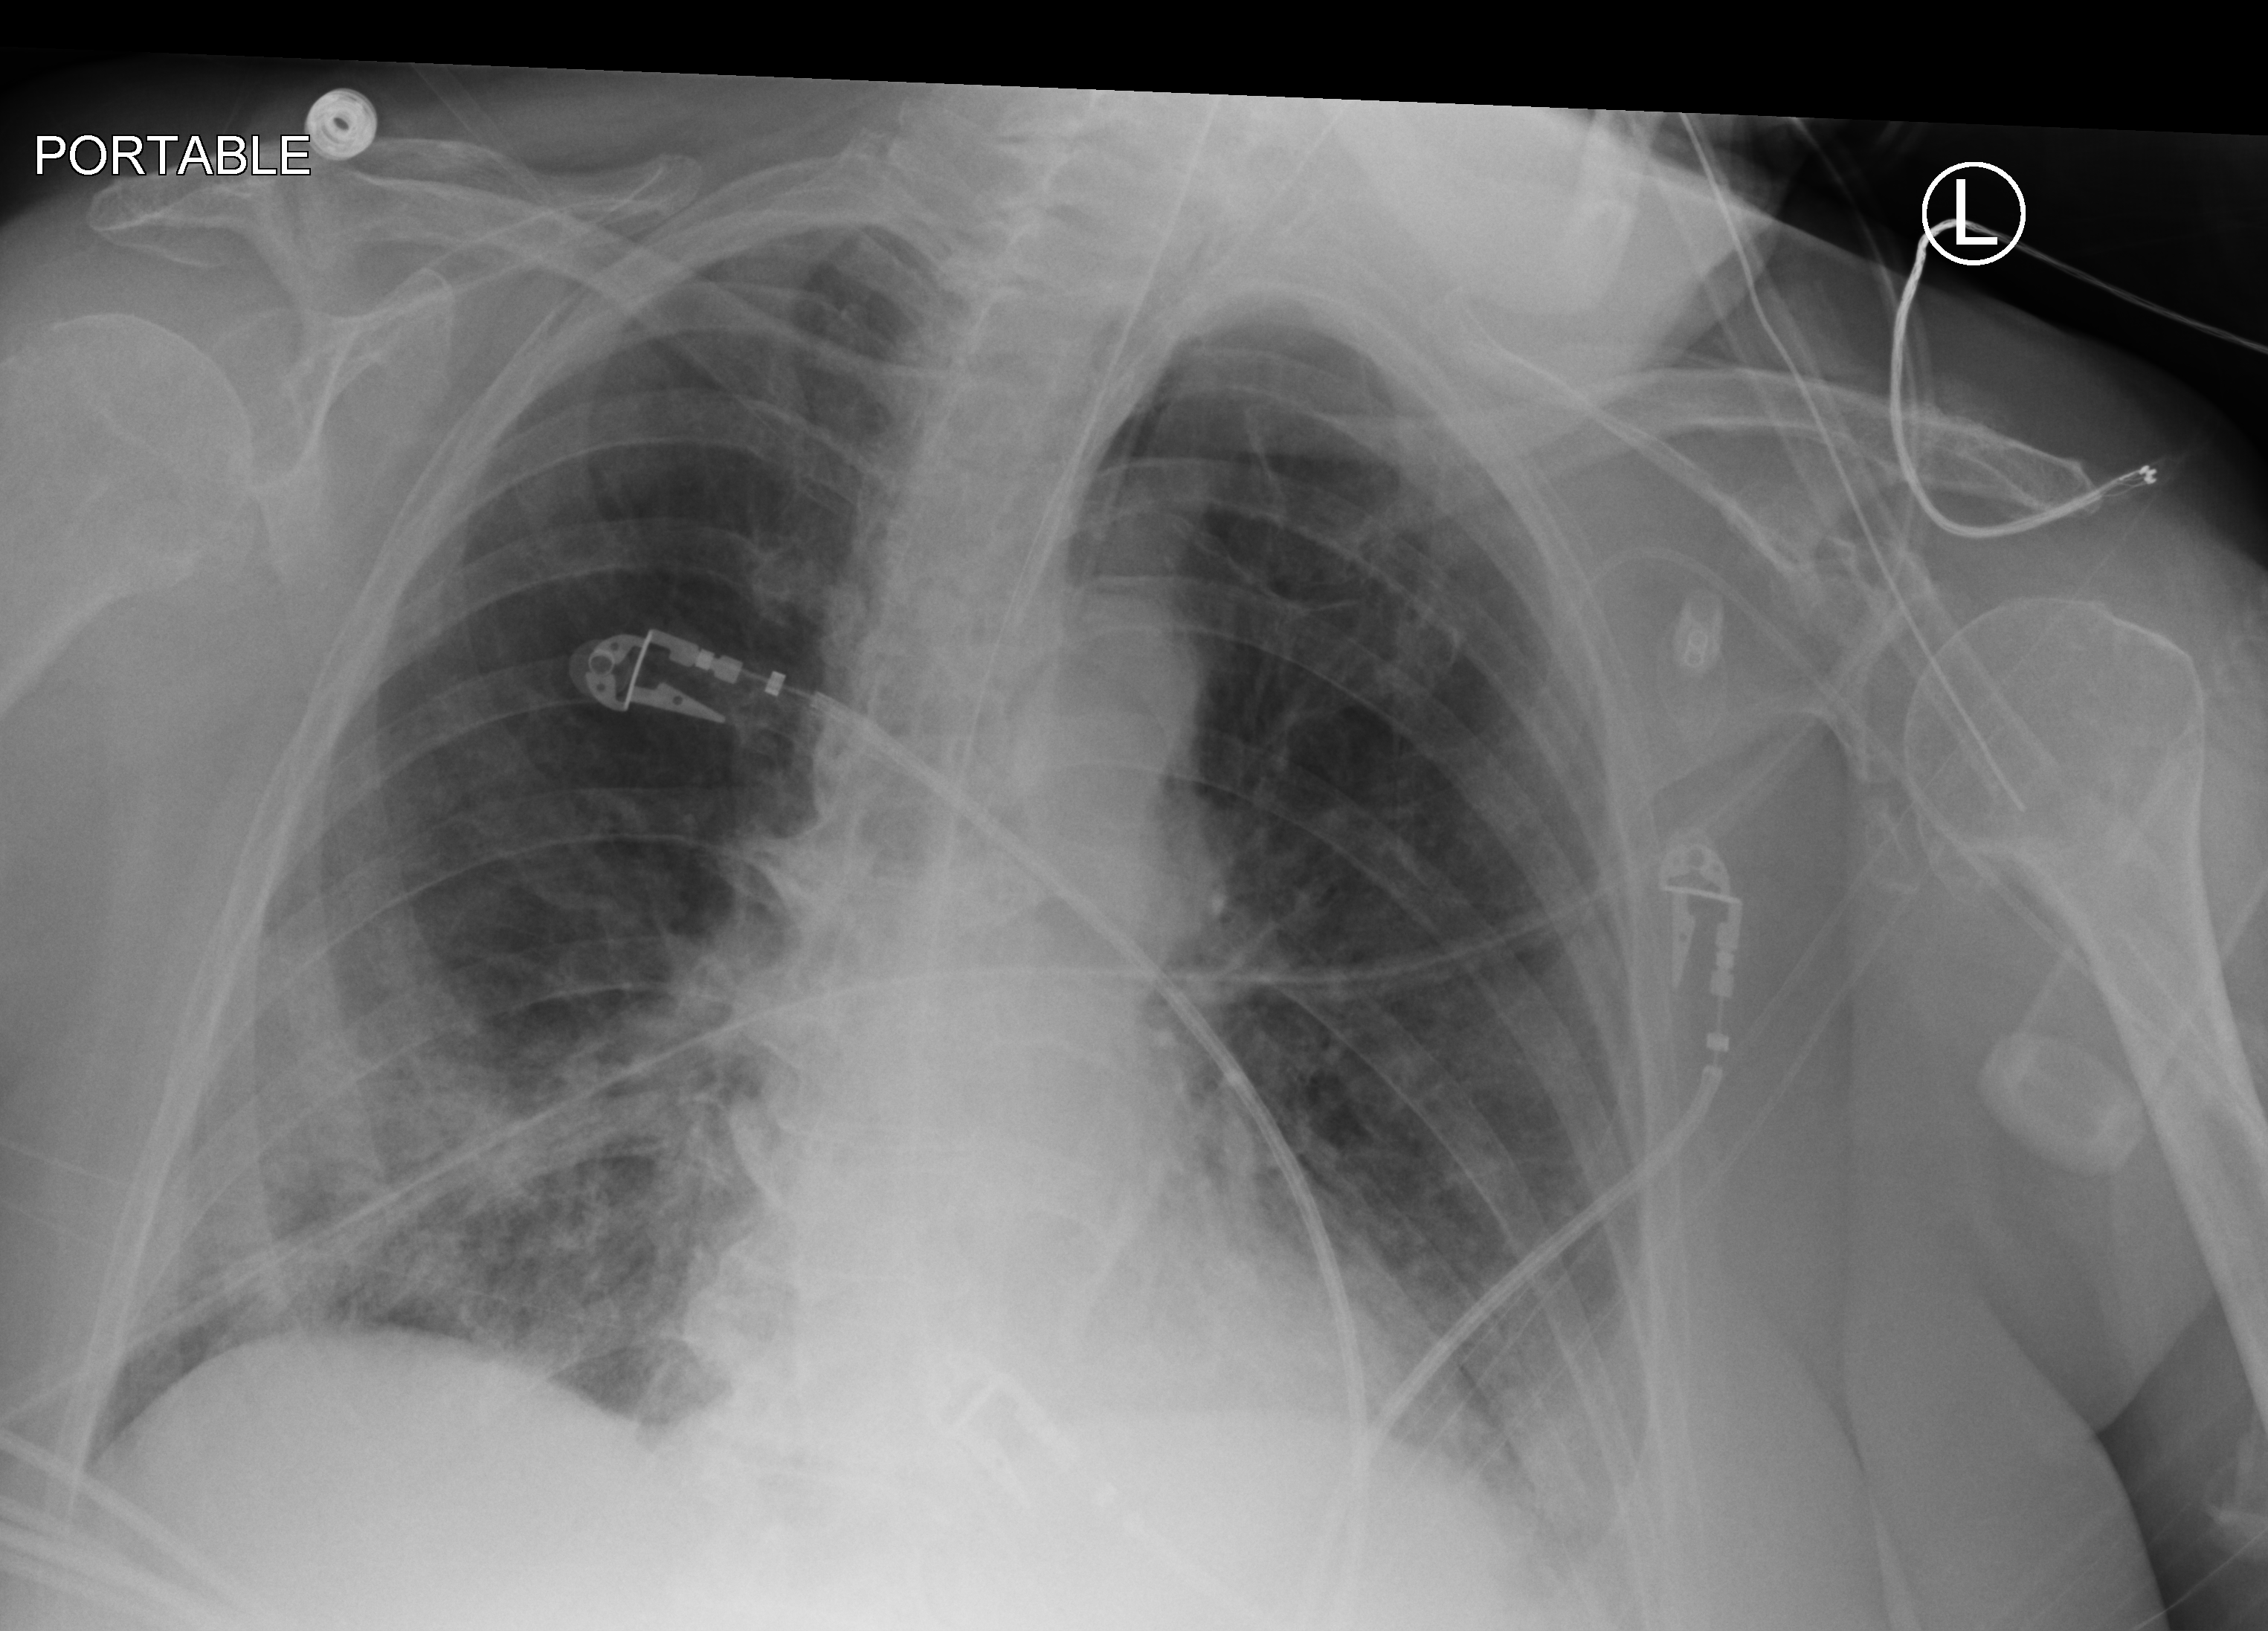
Chest X-ray (portable); anteroposterior (AP) projection. Female patient hospitalised with COVID-19, age 75–90 years.
Hospital-stay facts (about this admission, not read from this image; timing relative to this image not recorded):
- admitted to intensive care during this hospital stay: no
- mechanically ventilated during this hospital stay: yes